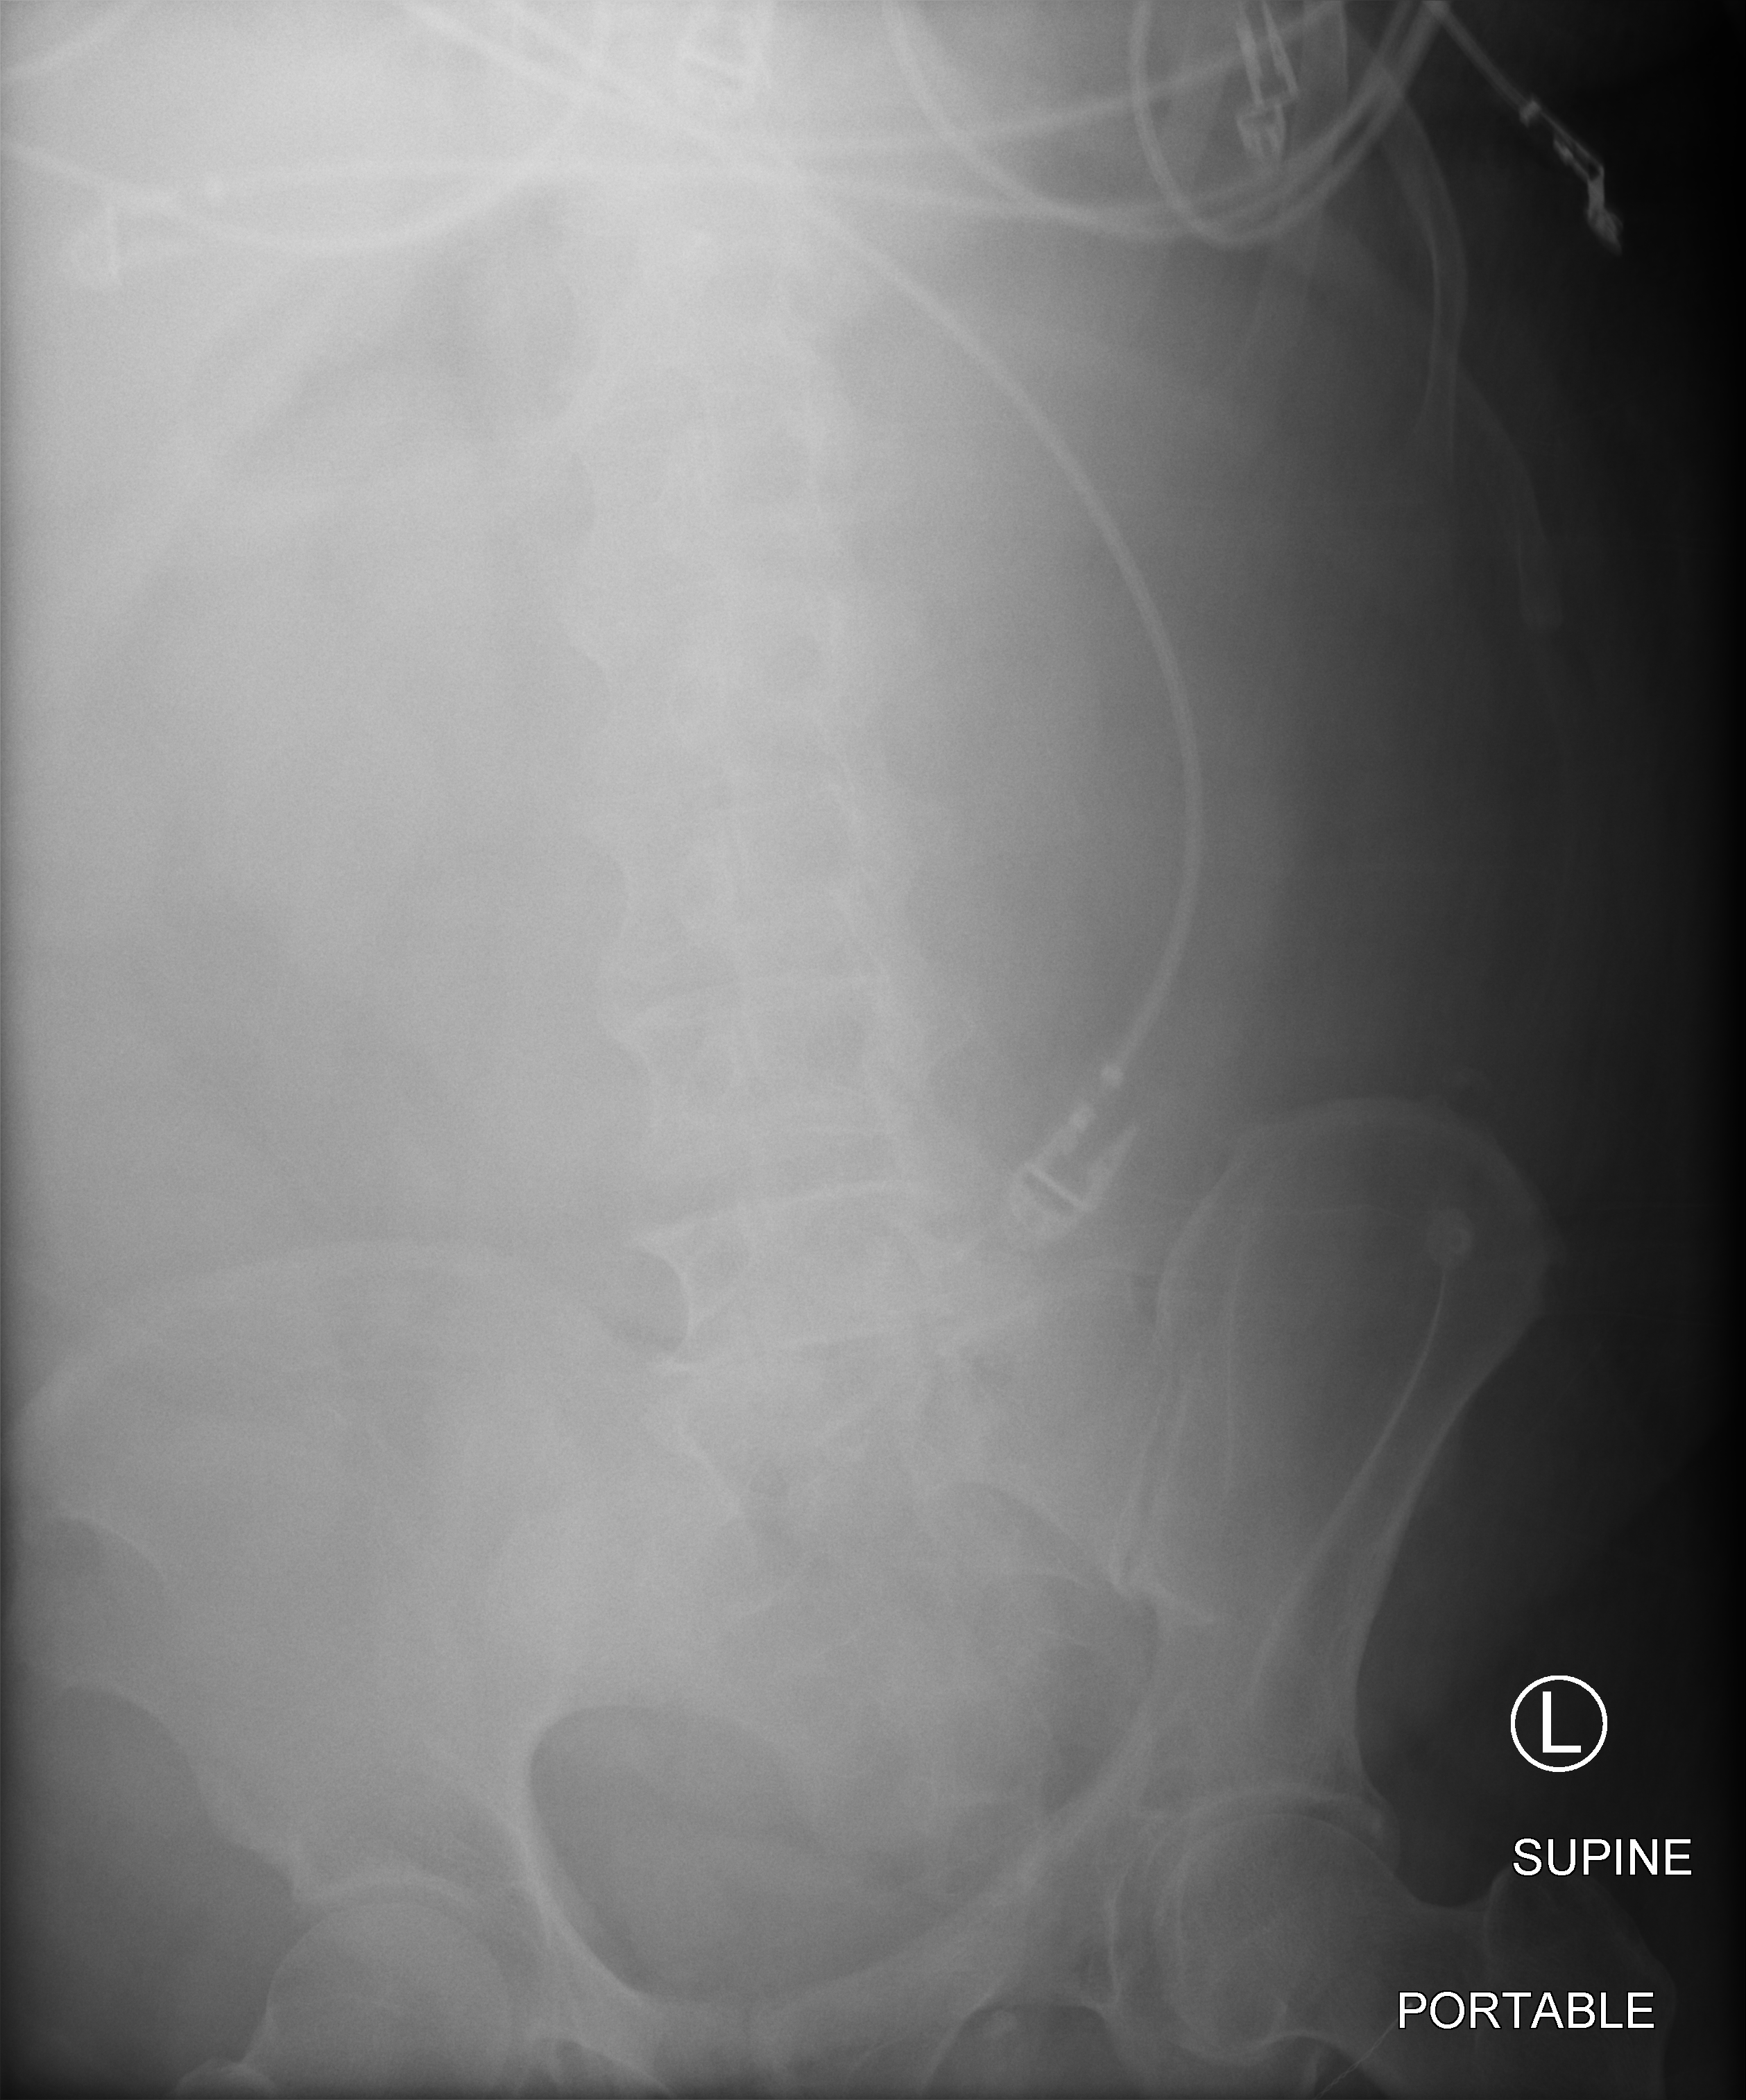
Bedside abdomen radiograph (computed radiography); anteroposterior (AP) projection. Patient hospitalised with COVID-19; male, aged 60–74 years.
From the hospital-stay record, not from the radiograph (when in the stay this image was taken is not recorded): mechanically ventilated during this hospital stay: yes.